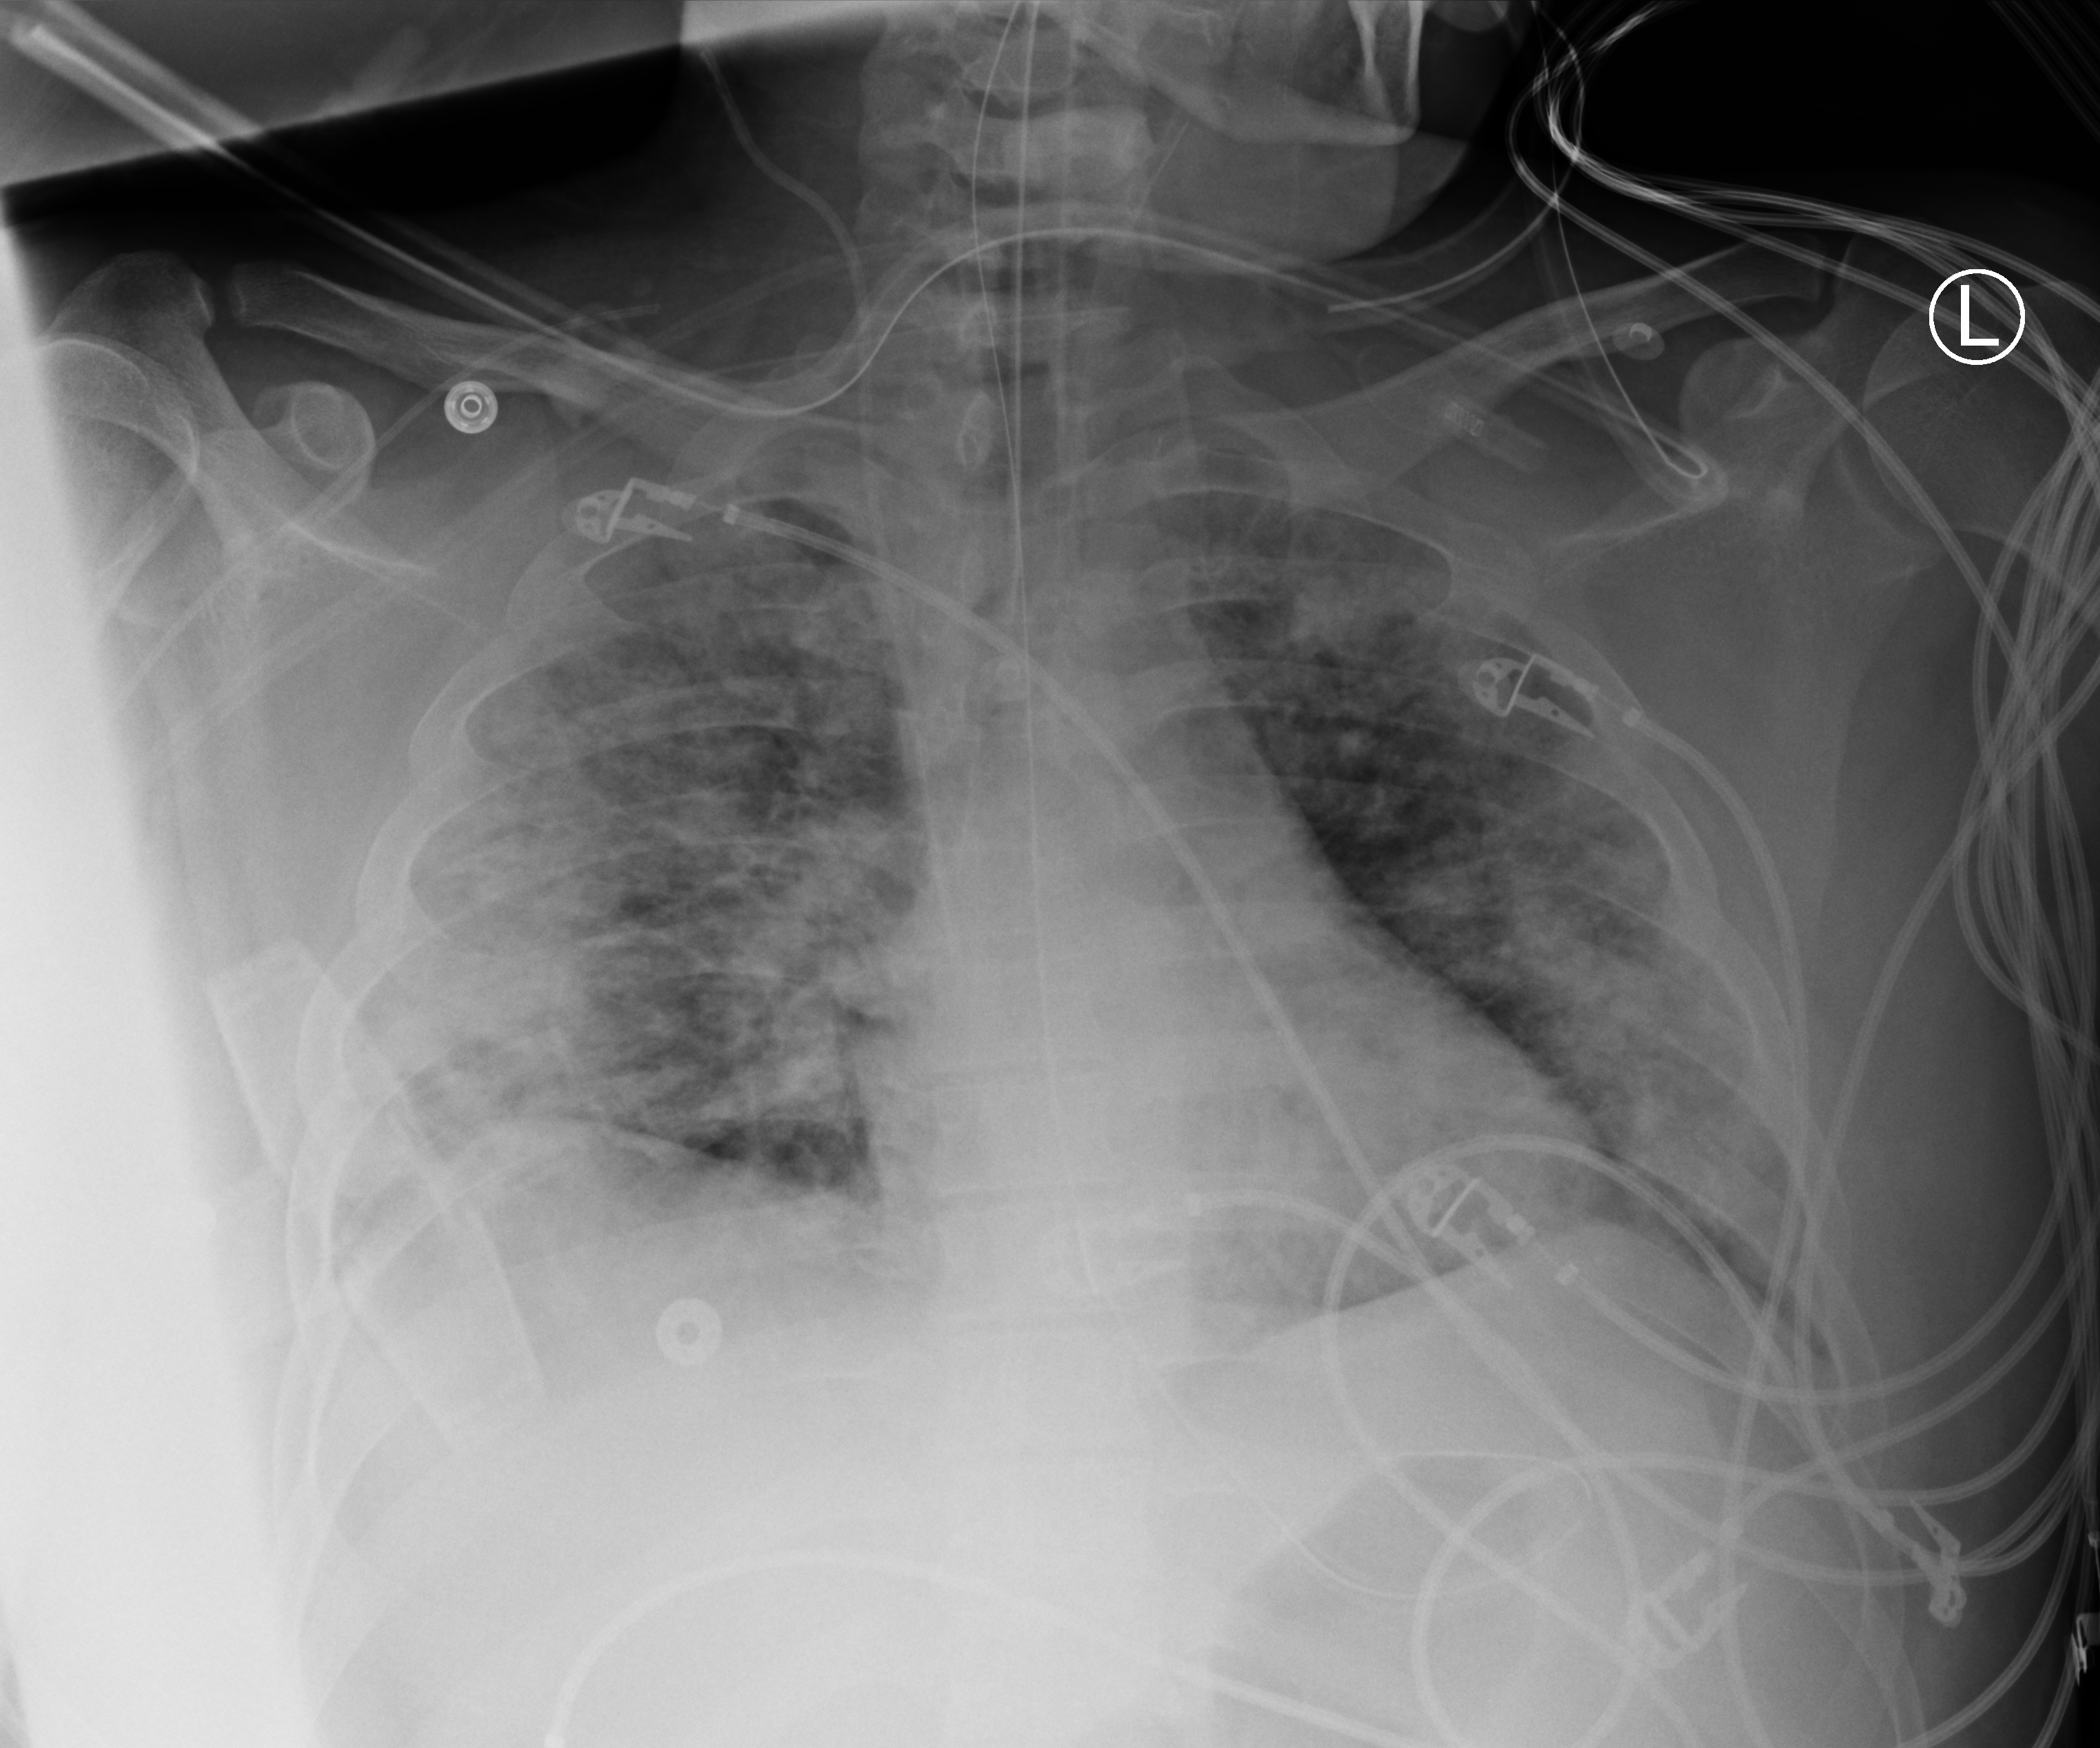
Chest X-ray (portable), anteroposterior (AP) projection. Male patient hospitalised with COVID-19, age 18–59 years.
From the hospital-stay record, not from the radiograph (when in the stay this image was taken is not recorded): length of hospital stay: 44 days.